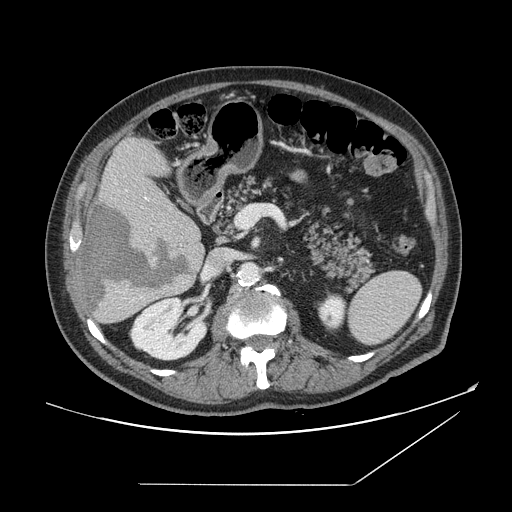
Contrast-enhanced abdominal CT, one axial slice. Intravenous contrast given. Soft-tissue window (W 400 / L 40 HU). 512 × 512 image matrix. Male patient, age 80 years. Case-level facts recorded for this patient, not image findings: diagnosis: colorectal cancer liver metastases, imaged before liver resection; multiple liver metastases: no; largest metastasis: 2.2 cm; chemotherapy before resection: no.
Structures marked on this image (expert manual segmentation):
- hepatic veins: box from (x=146, y=198) to (x=148, y=200) px
- liver: (x=78, y=138)–(x=206, y=325)
- planned liver remnant (the part of the liver to remain after resection): (x=102, y=137)–(x=199, y=234)
- liver metastasis: (x=81, y=201)–(x=191, y=314)